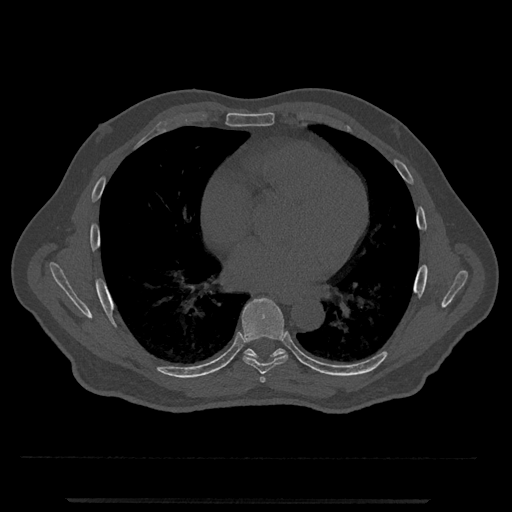
CT including the spine, one axial slice. Position 666 of 797 along the scan axis. 120 kVp. Bone window (W 1800 / L 400 HU). 0.5 mm slice thickness. 512 × 512 image matrix, field of view 419 × 419 mm. Male patient, age 63 years. From the clinical record (not read from this slice): primary cancer: prostate.
Outlined on this slice (semi-automatic segmentation, software-assisted and operator-edited):
- T6 vertebra: box from (x=260, y=376) to (x=266, y=383) px
- T7 vertebra: (x=242, y=297)–(x=288, y=374)
- T8 vertebra: (x=244, y=348)–(x=286, y=359)